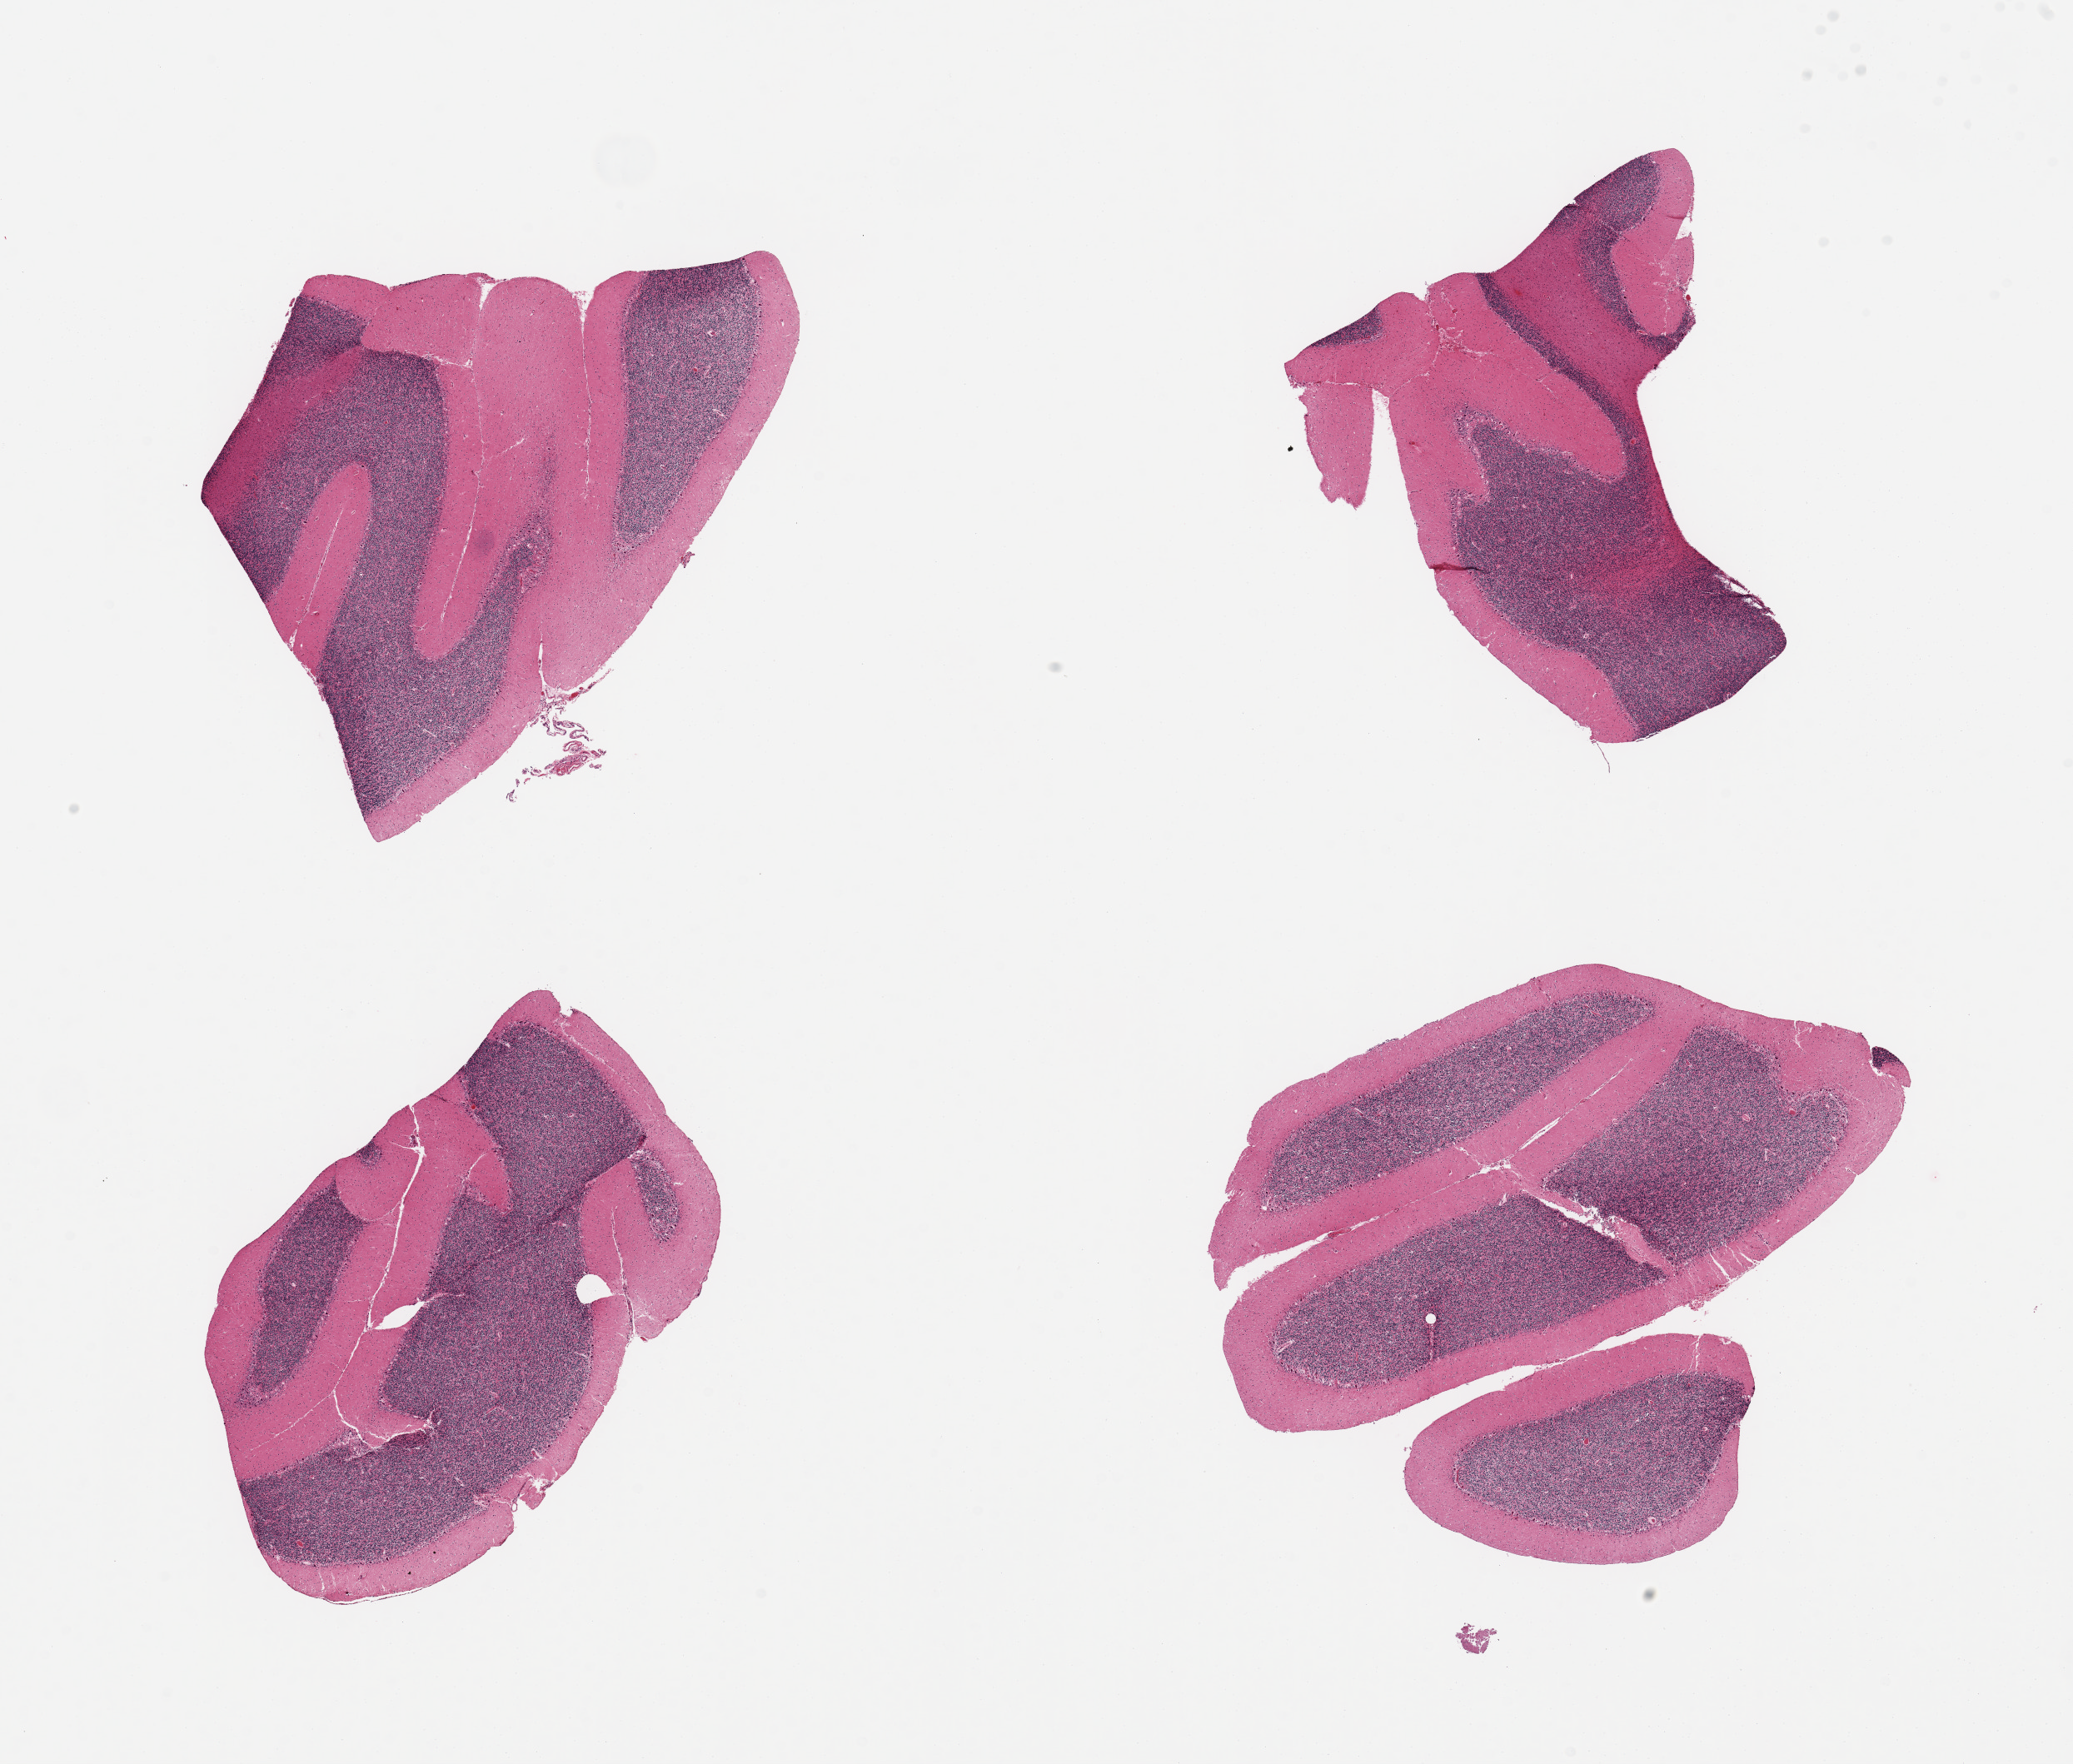
Digitized haematoxylin and eosin-stained section, low-resolution overview of the scanned area, about 19.7 x 16.8 mm (acquisition: 20x scan). PAXgene-fixed paraffin-embedded (PFPE) section. Section of cerebellum (target tissue). Donor tissue sample. Female donor.
- review note (as recorded): 4 pieces